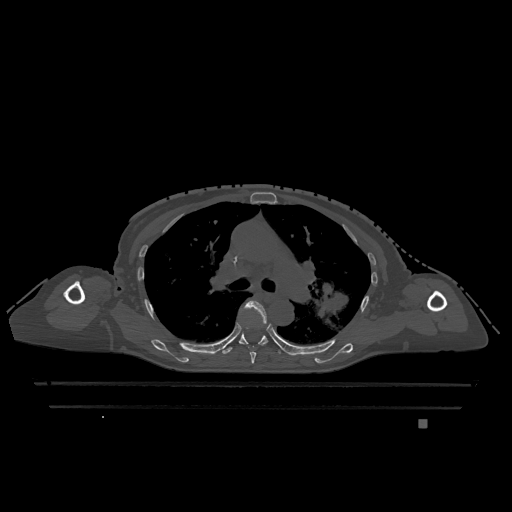
CT including the spine, one axial slice. Position 812 of 1317 along the scan axis. Bone window (W 1800 / L 400 HU). 0.5 mm slice thickness. 512 × 512 image matrix, field of view 500 × 500 mm. Patient: female, 74 years. Case-level facts recorded for this patient, not image findings: primary cancer: lung; vertebrae with lytic lesions (as recorded): T1, T4, T5, T6, L4, L5.
Annotated regions visible in this slice (semi-automatic segmentation, software-assisted and operator-edited):
- T5 vertebra: box from (x=243, y=301) to (x=267, y=364) px
- T6 vertebra: (x=222, y=327)–(x=281, y=354)